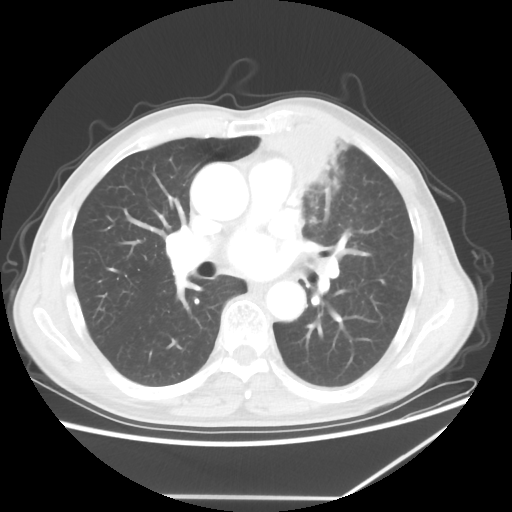
Chest CT, one axial slice. Position 34 of 64 along the scan axis. 100 kVp. Lung window (W 1500 / L -600 HU). 5 mm slice thickness. 512 × 512 image matrix. Male patient, age 64 years. From the clinical record (not read from this slice): clinical TNM (as recorded): T1c N1 M1; histopathological grade: G2.
Outlined on this slice (rectangle marked by the reading radiologist):
- lung tumour (recorded histology: squamous cell carcinoma): bounding box (x1, y1, x2, y2) in pixels: (261, 121, 367, 200)